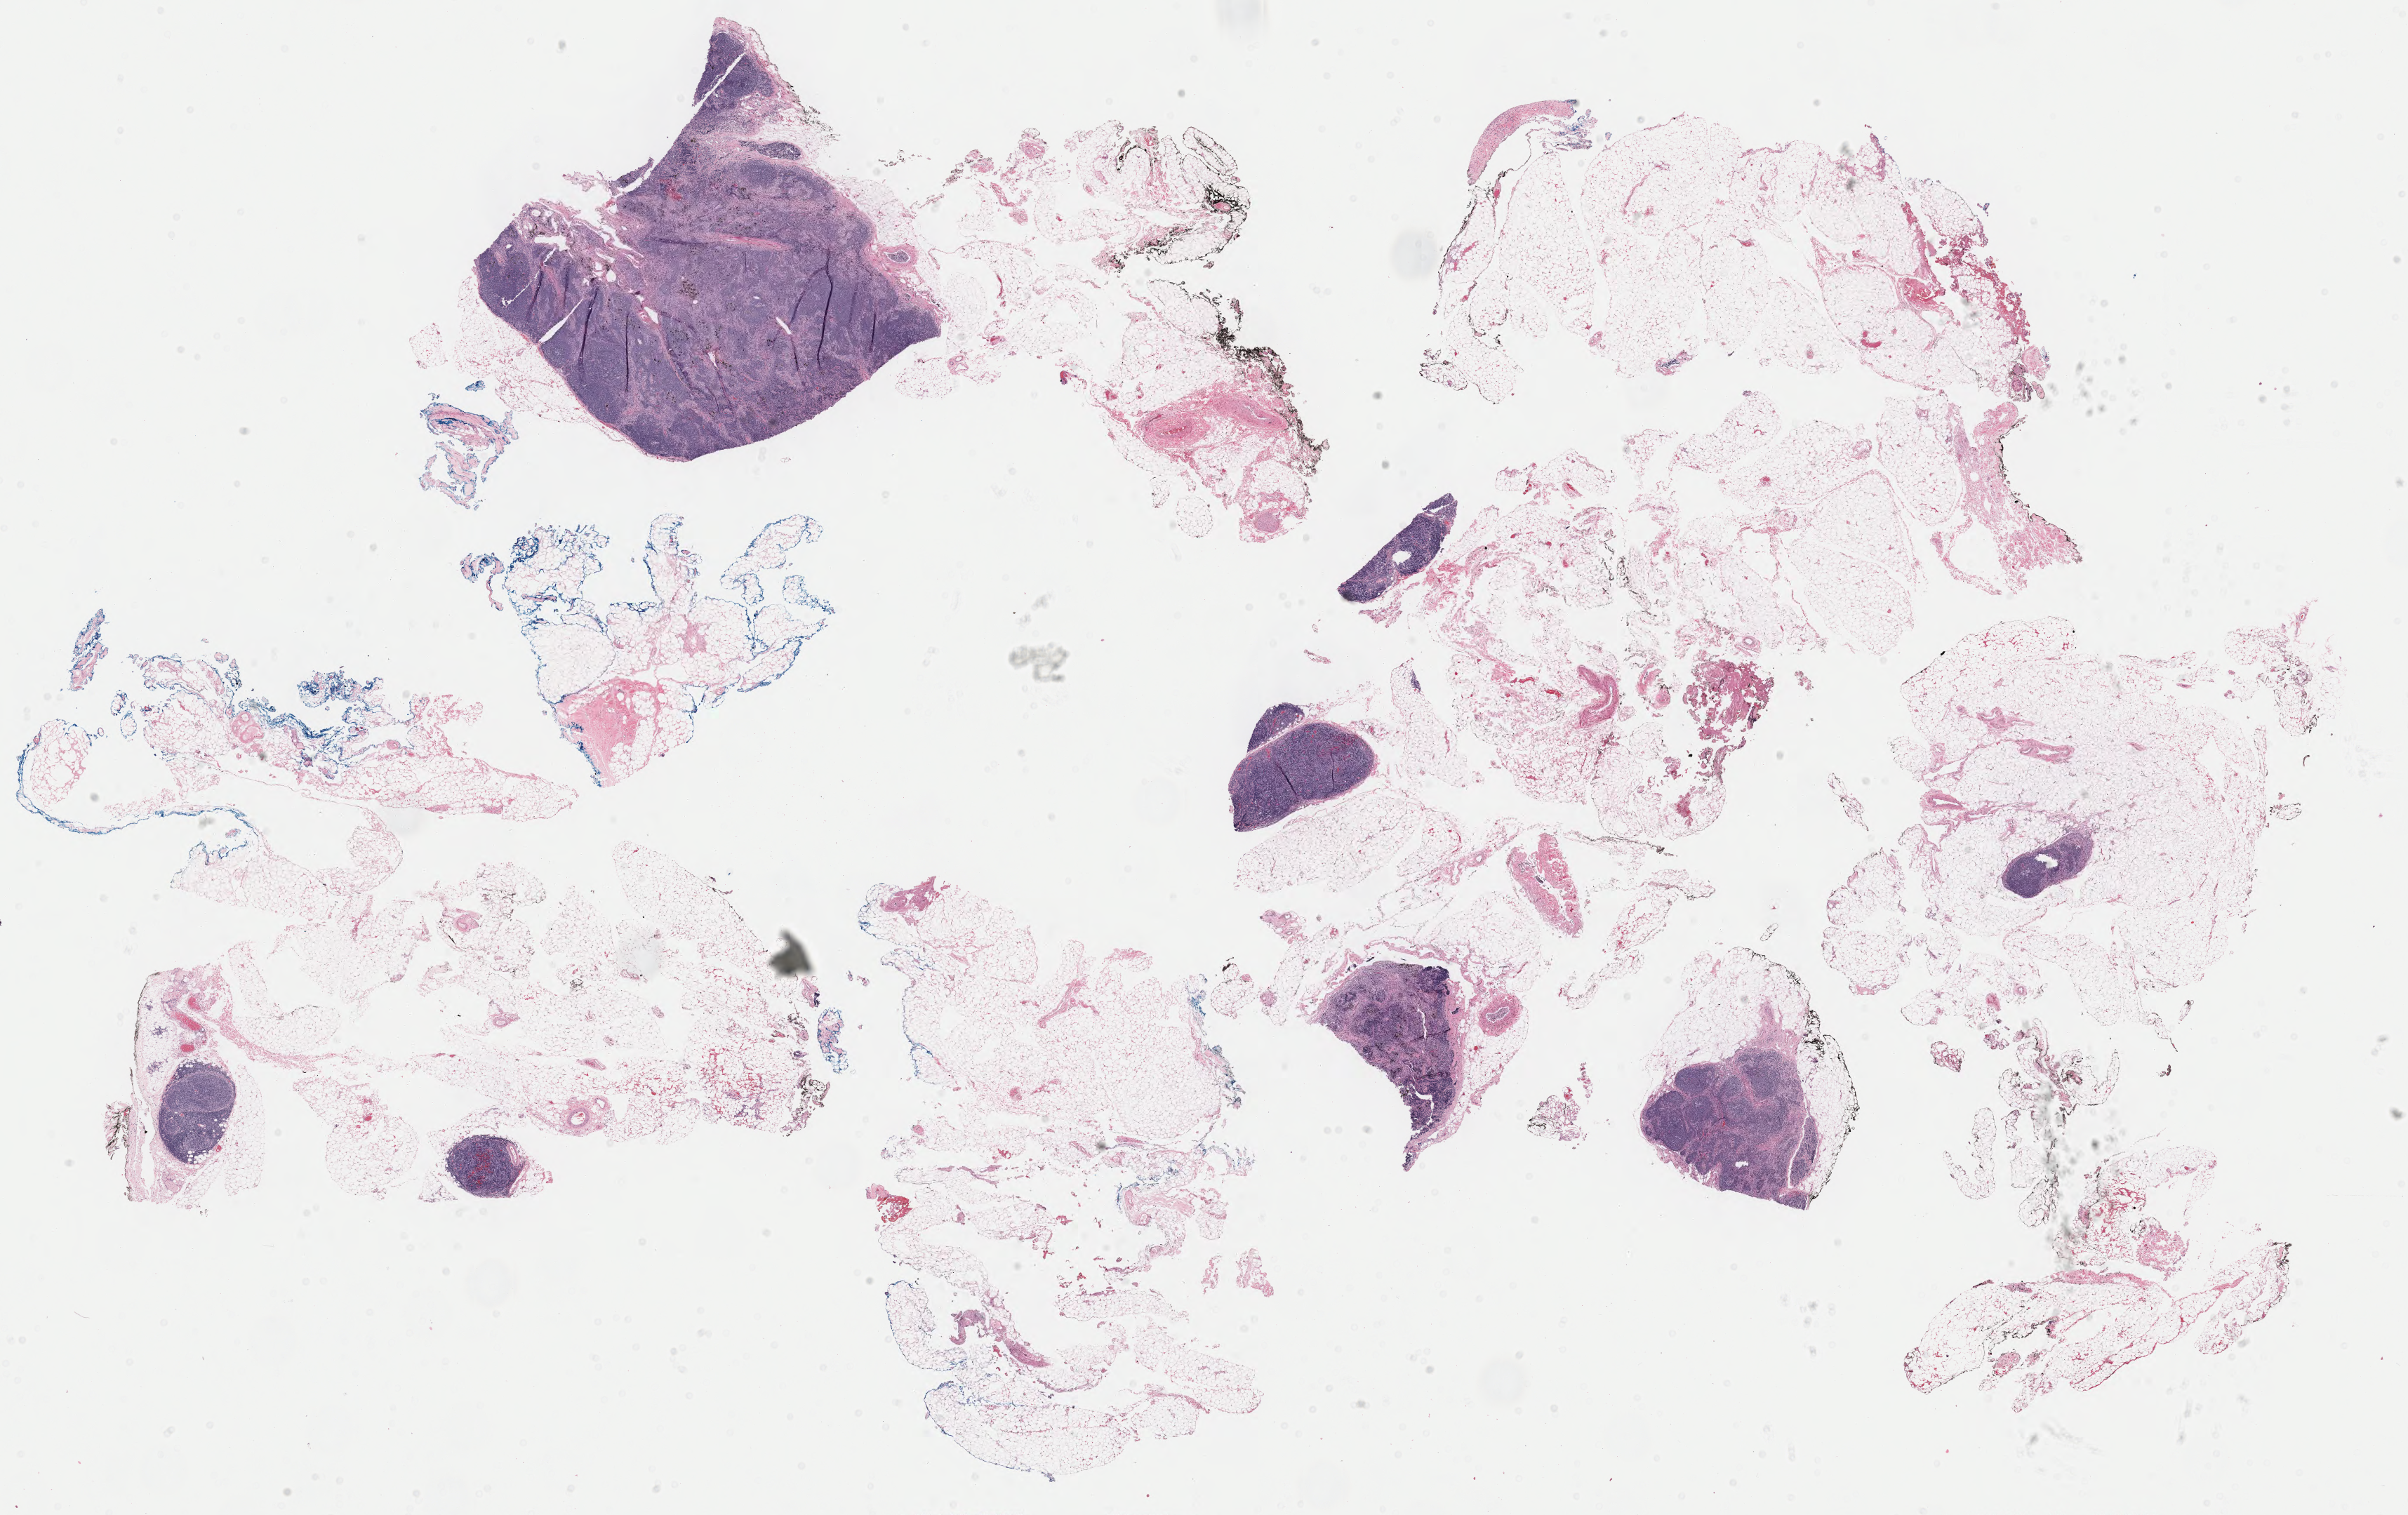
Digitized Hematoxylin and eosin (H&E) stained tissue section (whole slide) — whole scanned area (about 27.2 x 17.1 mm) shown as a low-resolution overview, FFPE section, thymus, primary tumour sample. Female patient; age at initial diagnosis 43 years.
Pathologic diagnosis: Thymoma, type B2, malignant.